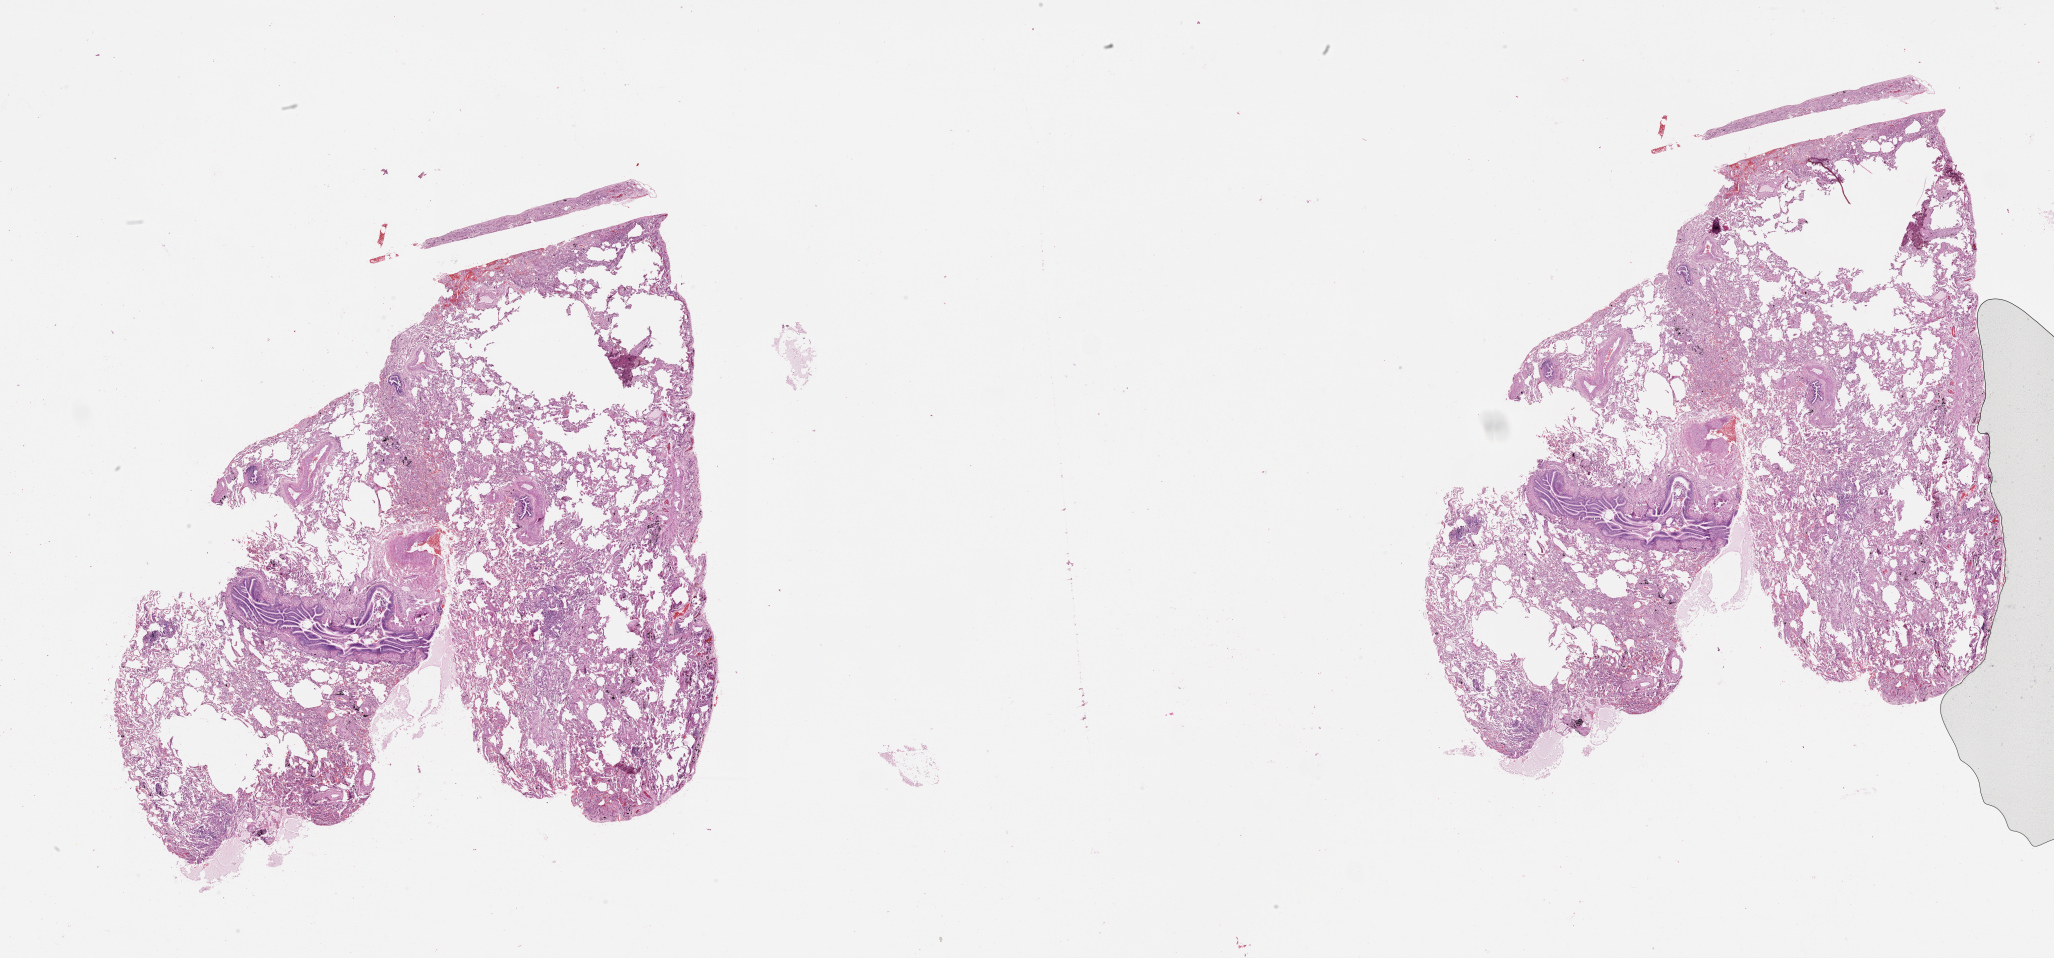
H&E-stained whole-slide image, shown as a low-resolution overview of the whole scanned area (about 33.1 x 15.4 mm, slide scanned at 20x); lung, tissue type not recorded.
* patient diagnosis (cohort enrolment): squamous cell carcinoma (lung)